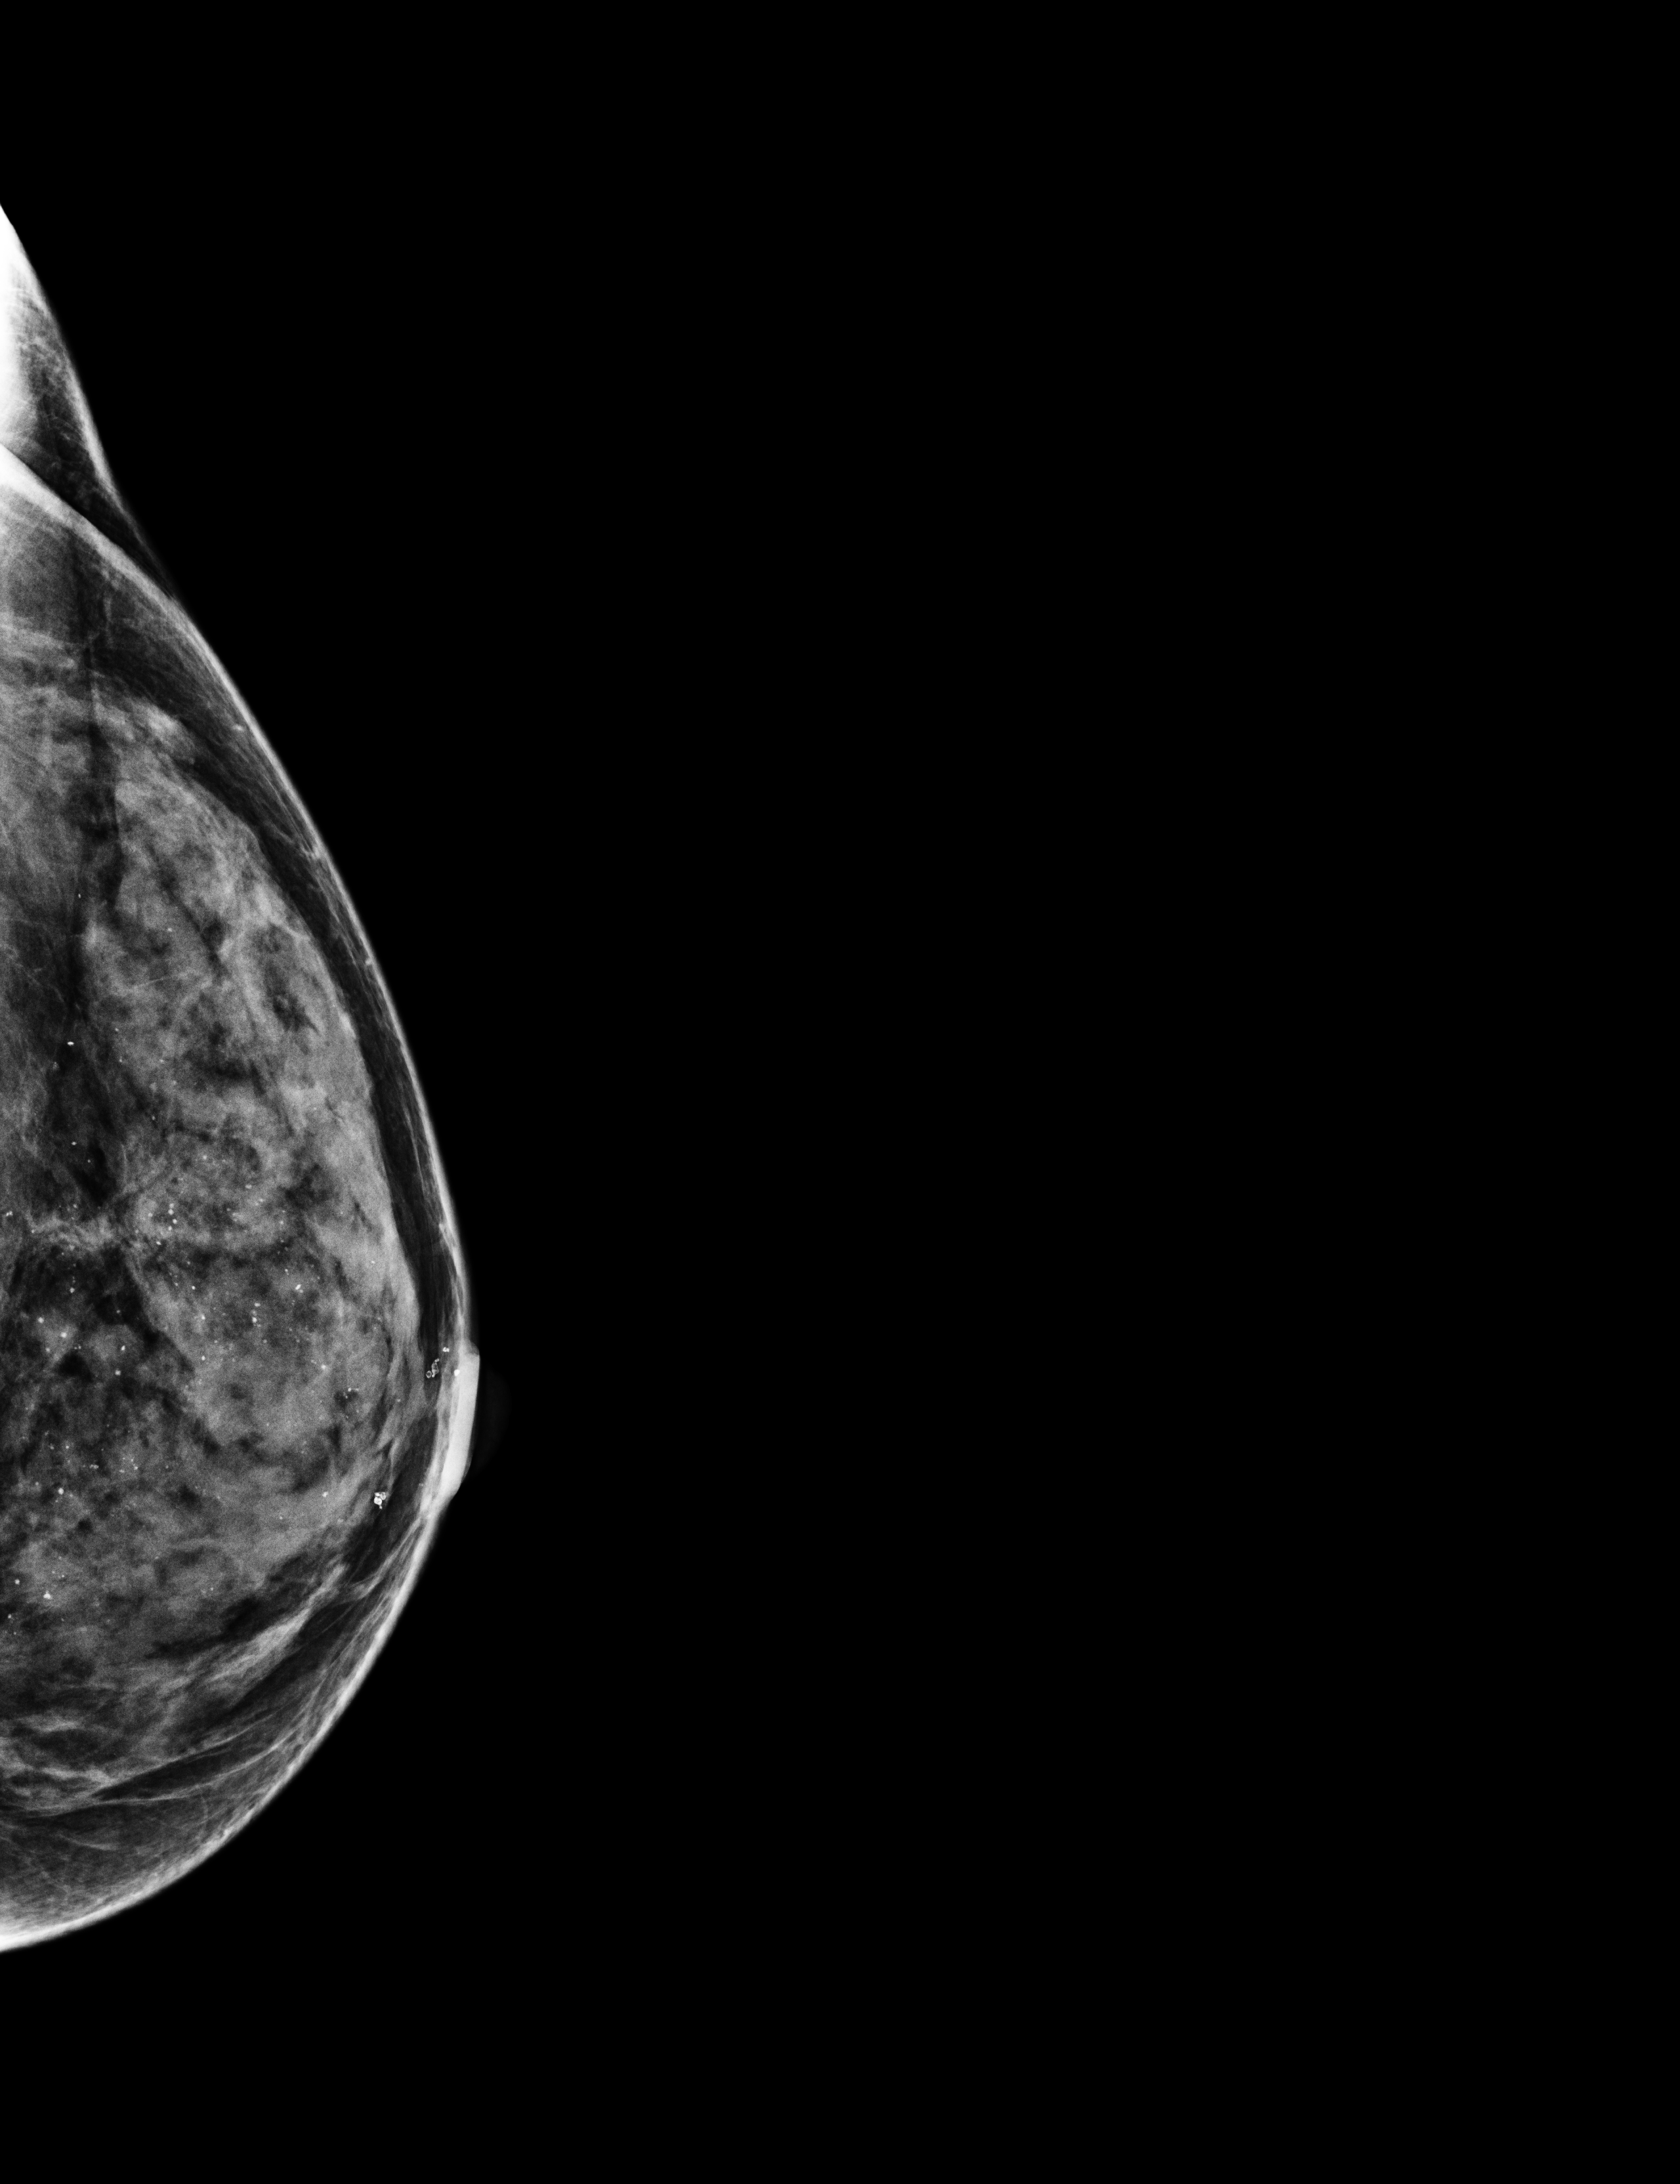
Digital mammogram (FFDM), left breast, laterally exaggerated craniocaudal (XCCL) view, screening examination, system: Selenia Dimensions. Patient aged 49 years (female).
BI-RADS breast density category at the screening exam (both breasts, scale 1–4): 4. Final BI-RADS assessment for this screening round (tomosynthesis exam, both breasts): category 2. Recall: no recall after this screen.